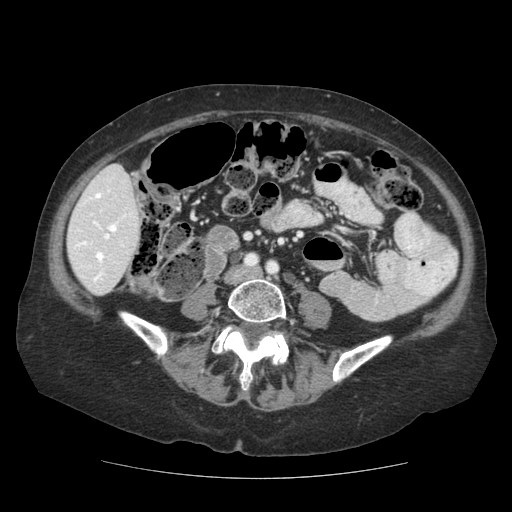
Contrast-enhanced abdominal CT (liver protocol), one axial slice; slice 30 of 111 in the series (ordered by position); reconstruction kernel STANDARD; 140 kVp; soft-tissue window (W 400 / L 40 HU); 2.5 mm slice thickness; 512 × 512 image matrix, field of view 360 × 360 mm. Case-level facts recorded for this patient, not image findings: diagnosis: hepatocellular carcinoma (patient treated with transarterial chemoembolisation; whether this scan precedes or follows treatment is not stated here); TNM stage (as recorded): Stage-I; Child-Pugh class: A; tumour differentiation: moderately-poorly differentiated; tumour nodularity: uninodular.
Structures marked on this image (semi-automatic segmentation, software-assisted and operator-edited):
- liver parenchyma outside the tumour (the mass and vessels are separate outlines, so this box may not span the whole liver): bounding box <66,164,140,295> (left, top, right, bottom; pixels)
- liver vessels: <73,190,126,282>